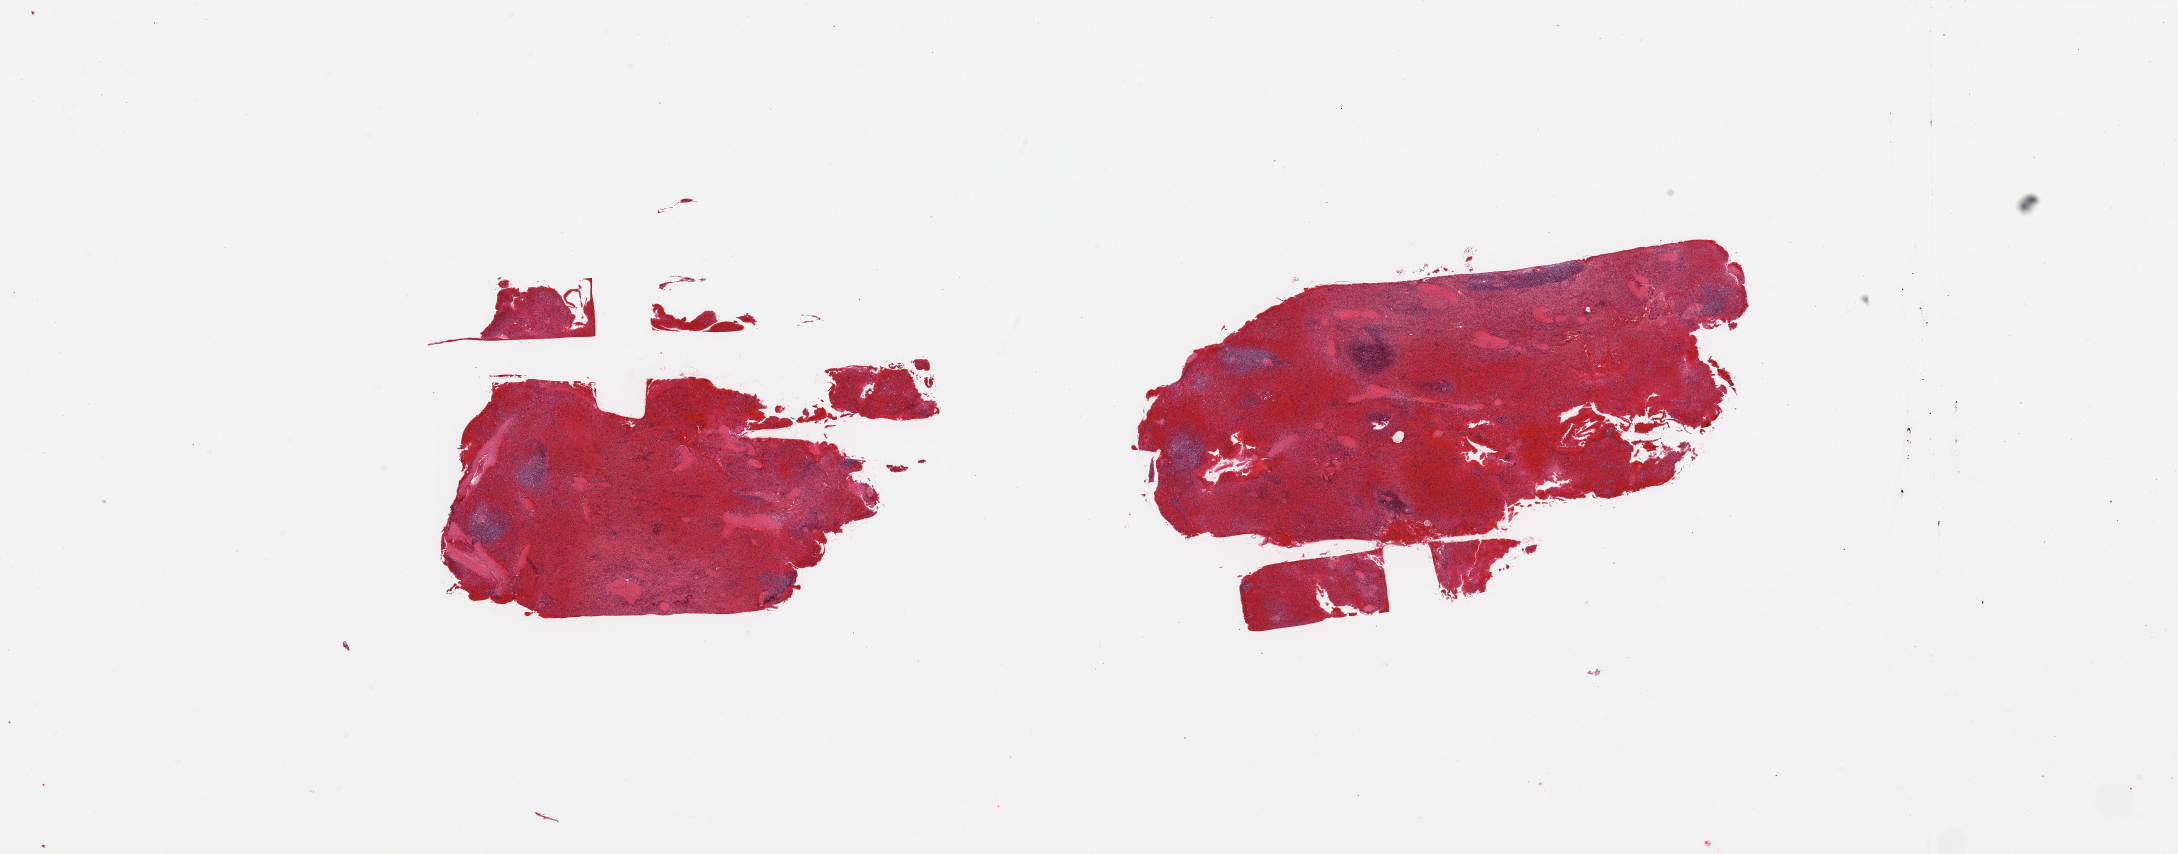
Whole-slide image, haematoxylin and eosin stain — whole scanned area (about 34.5 x 13.5 mm, acquisition: 20x scan) shown as a low-resolution overview. PAXgene-fixed, paraffin-embedded tissue. Target tissue: spleen. Tissue donor sample. Donor sex: male.
Pathologist's review note for this sample: 2 pieces, marked congestion/autolysis.